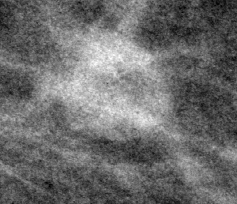
Cropped region of a digitized screen-film mammogram centred on a radiologist-marked abnormality, left breast, MLO view, BI-RADS breast density category 1 (scale 1–4).
- Finding: mass, shape lymph node, margins circumscribed; BI-RADS assessment category 2; benign without callback (not worked up further).